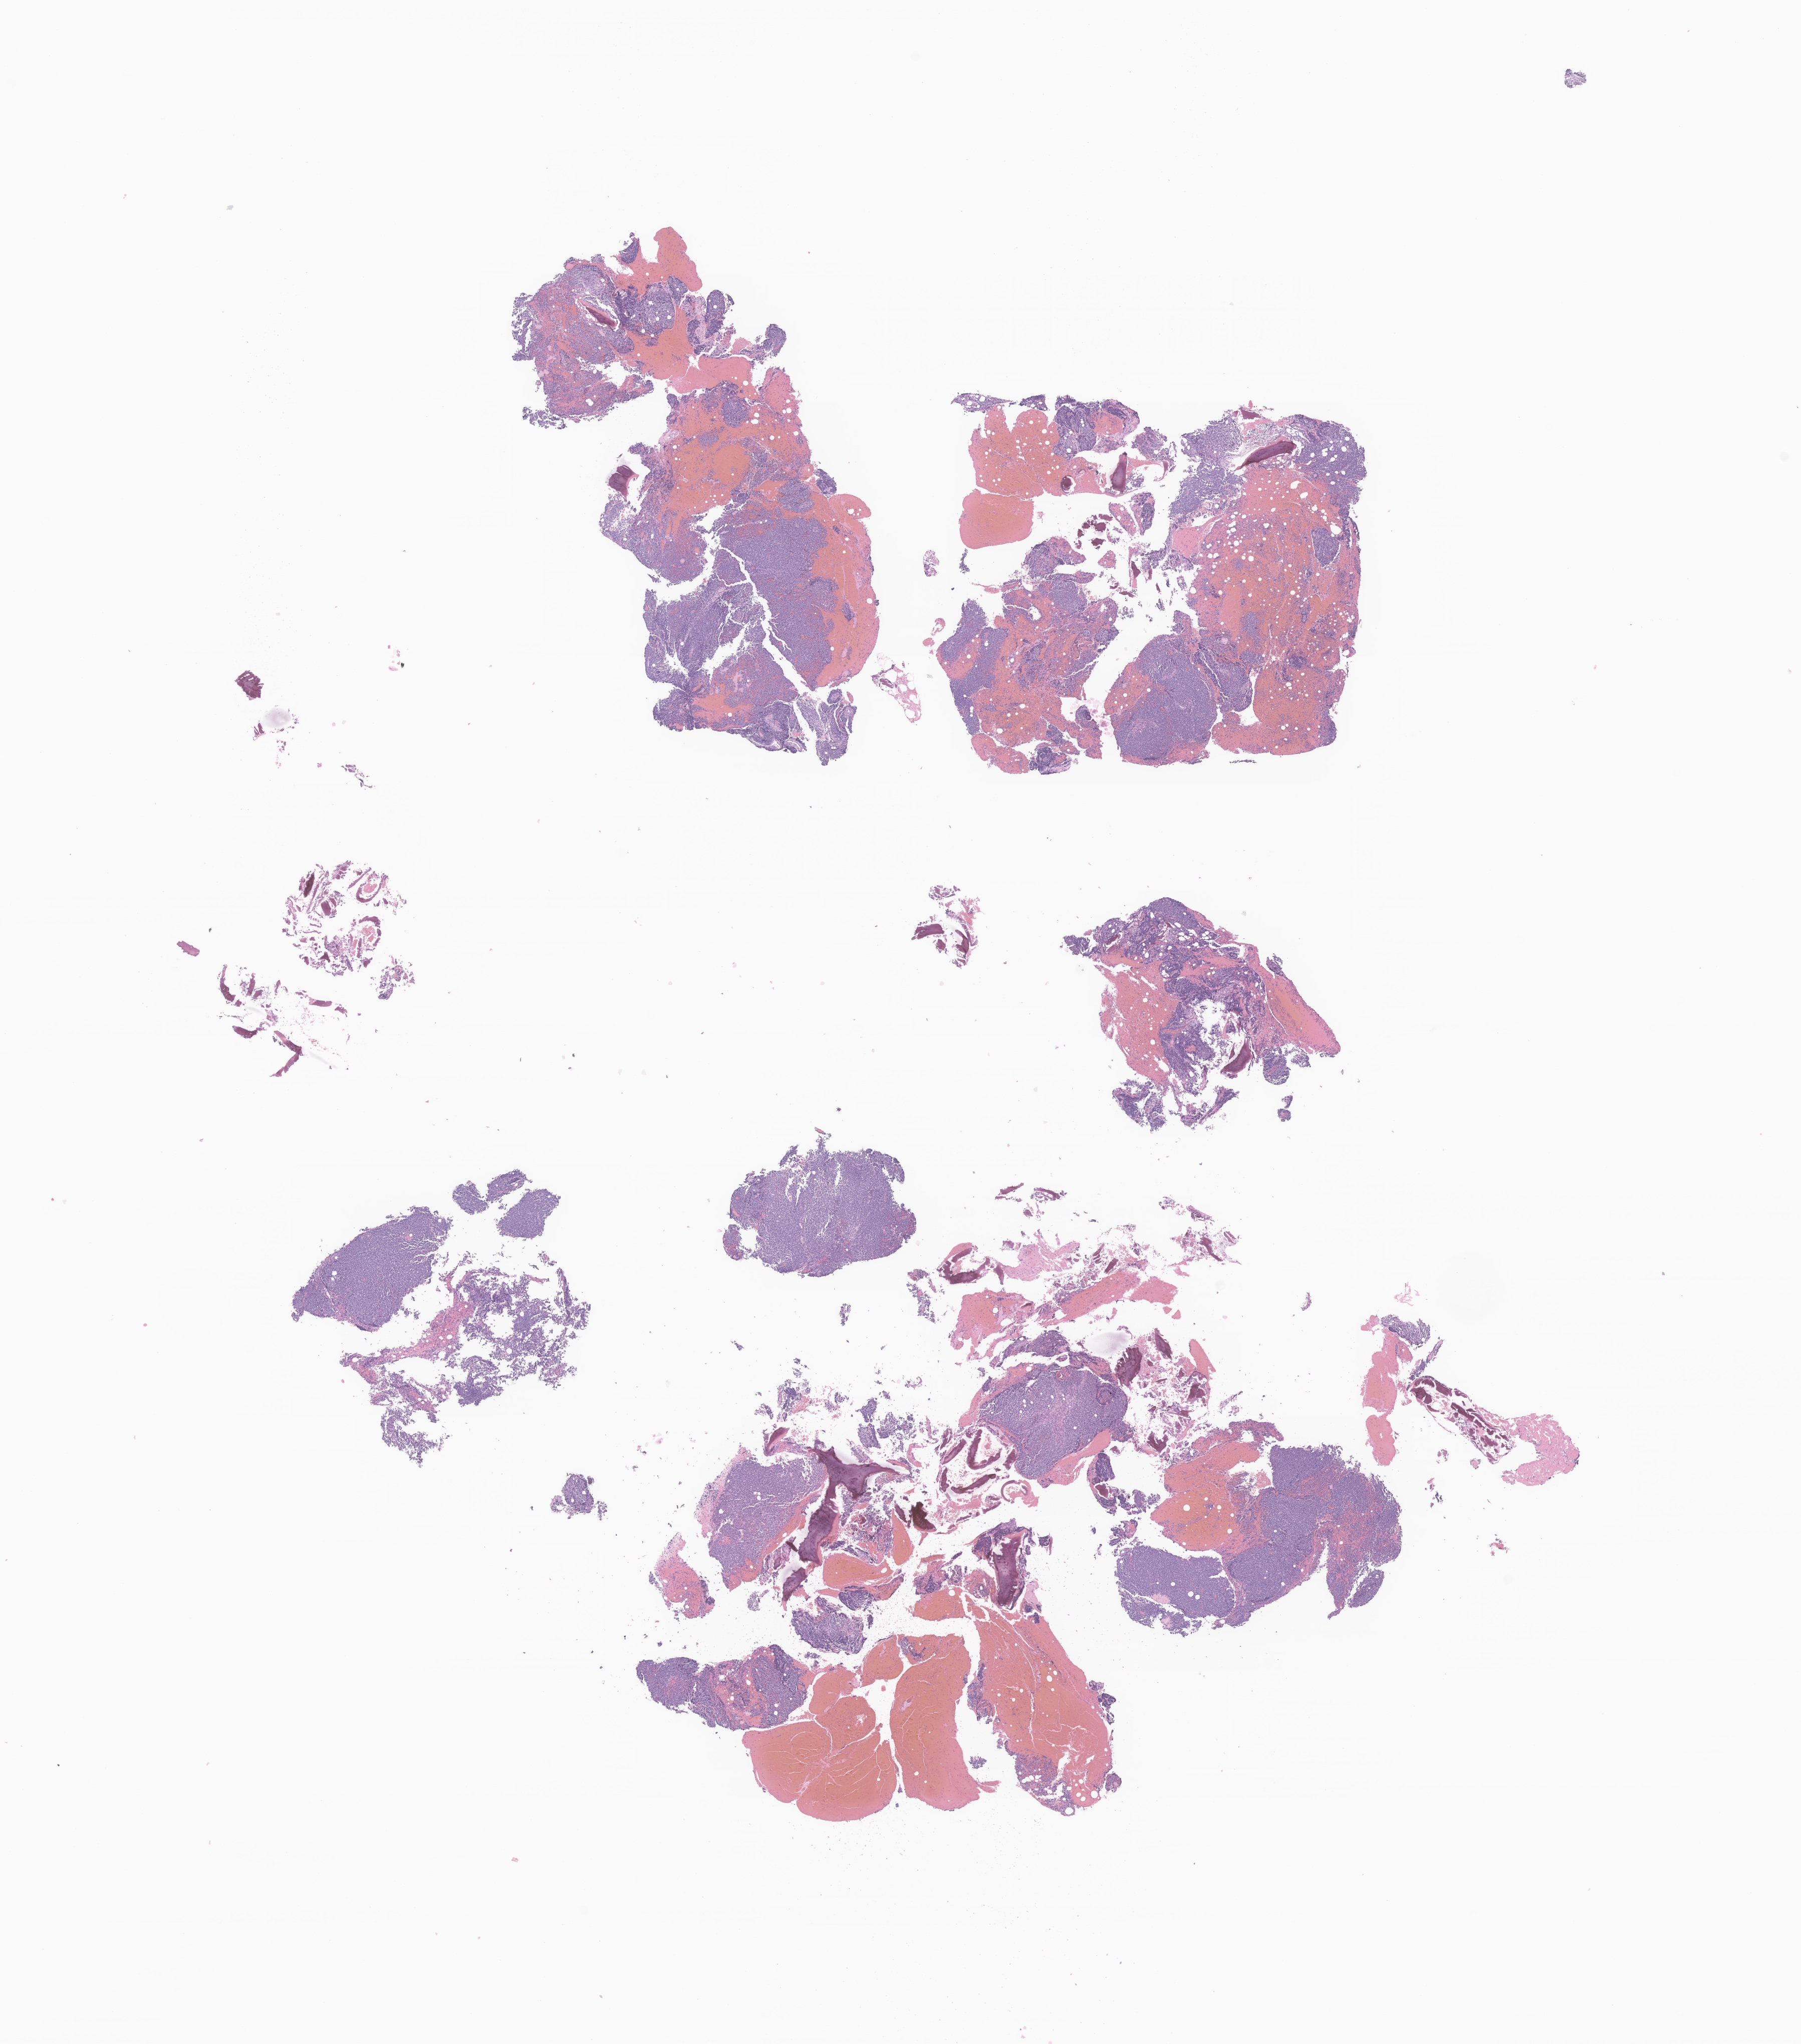
H&E whole-slide image of tumor tissue from the pelvis, shown as a low-resolution overview of the whole scanned area (about 15.2 x 17.2 mm), FFPE section. Male patient, age 513 days (about 1.4 years).
• recorded diagnosis: Alveolar rhabdomyosarcoma